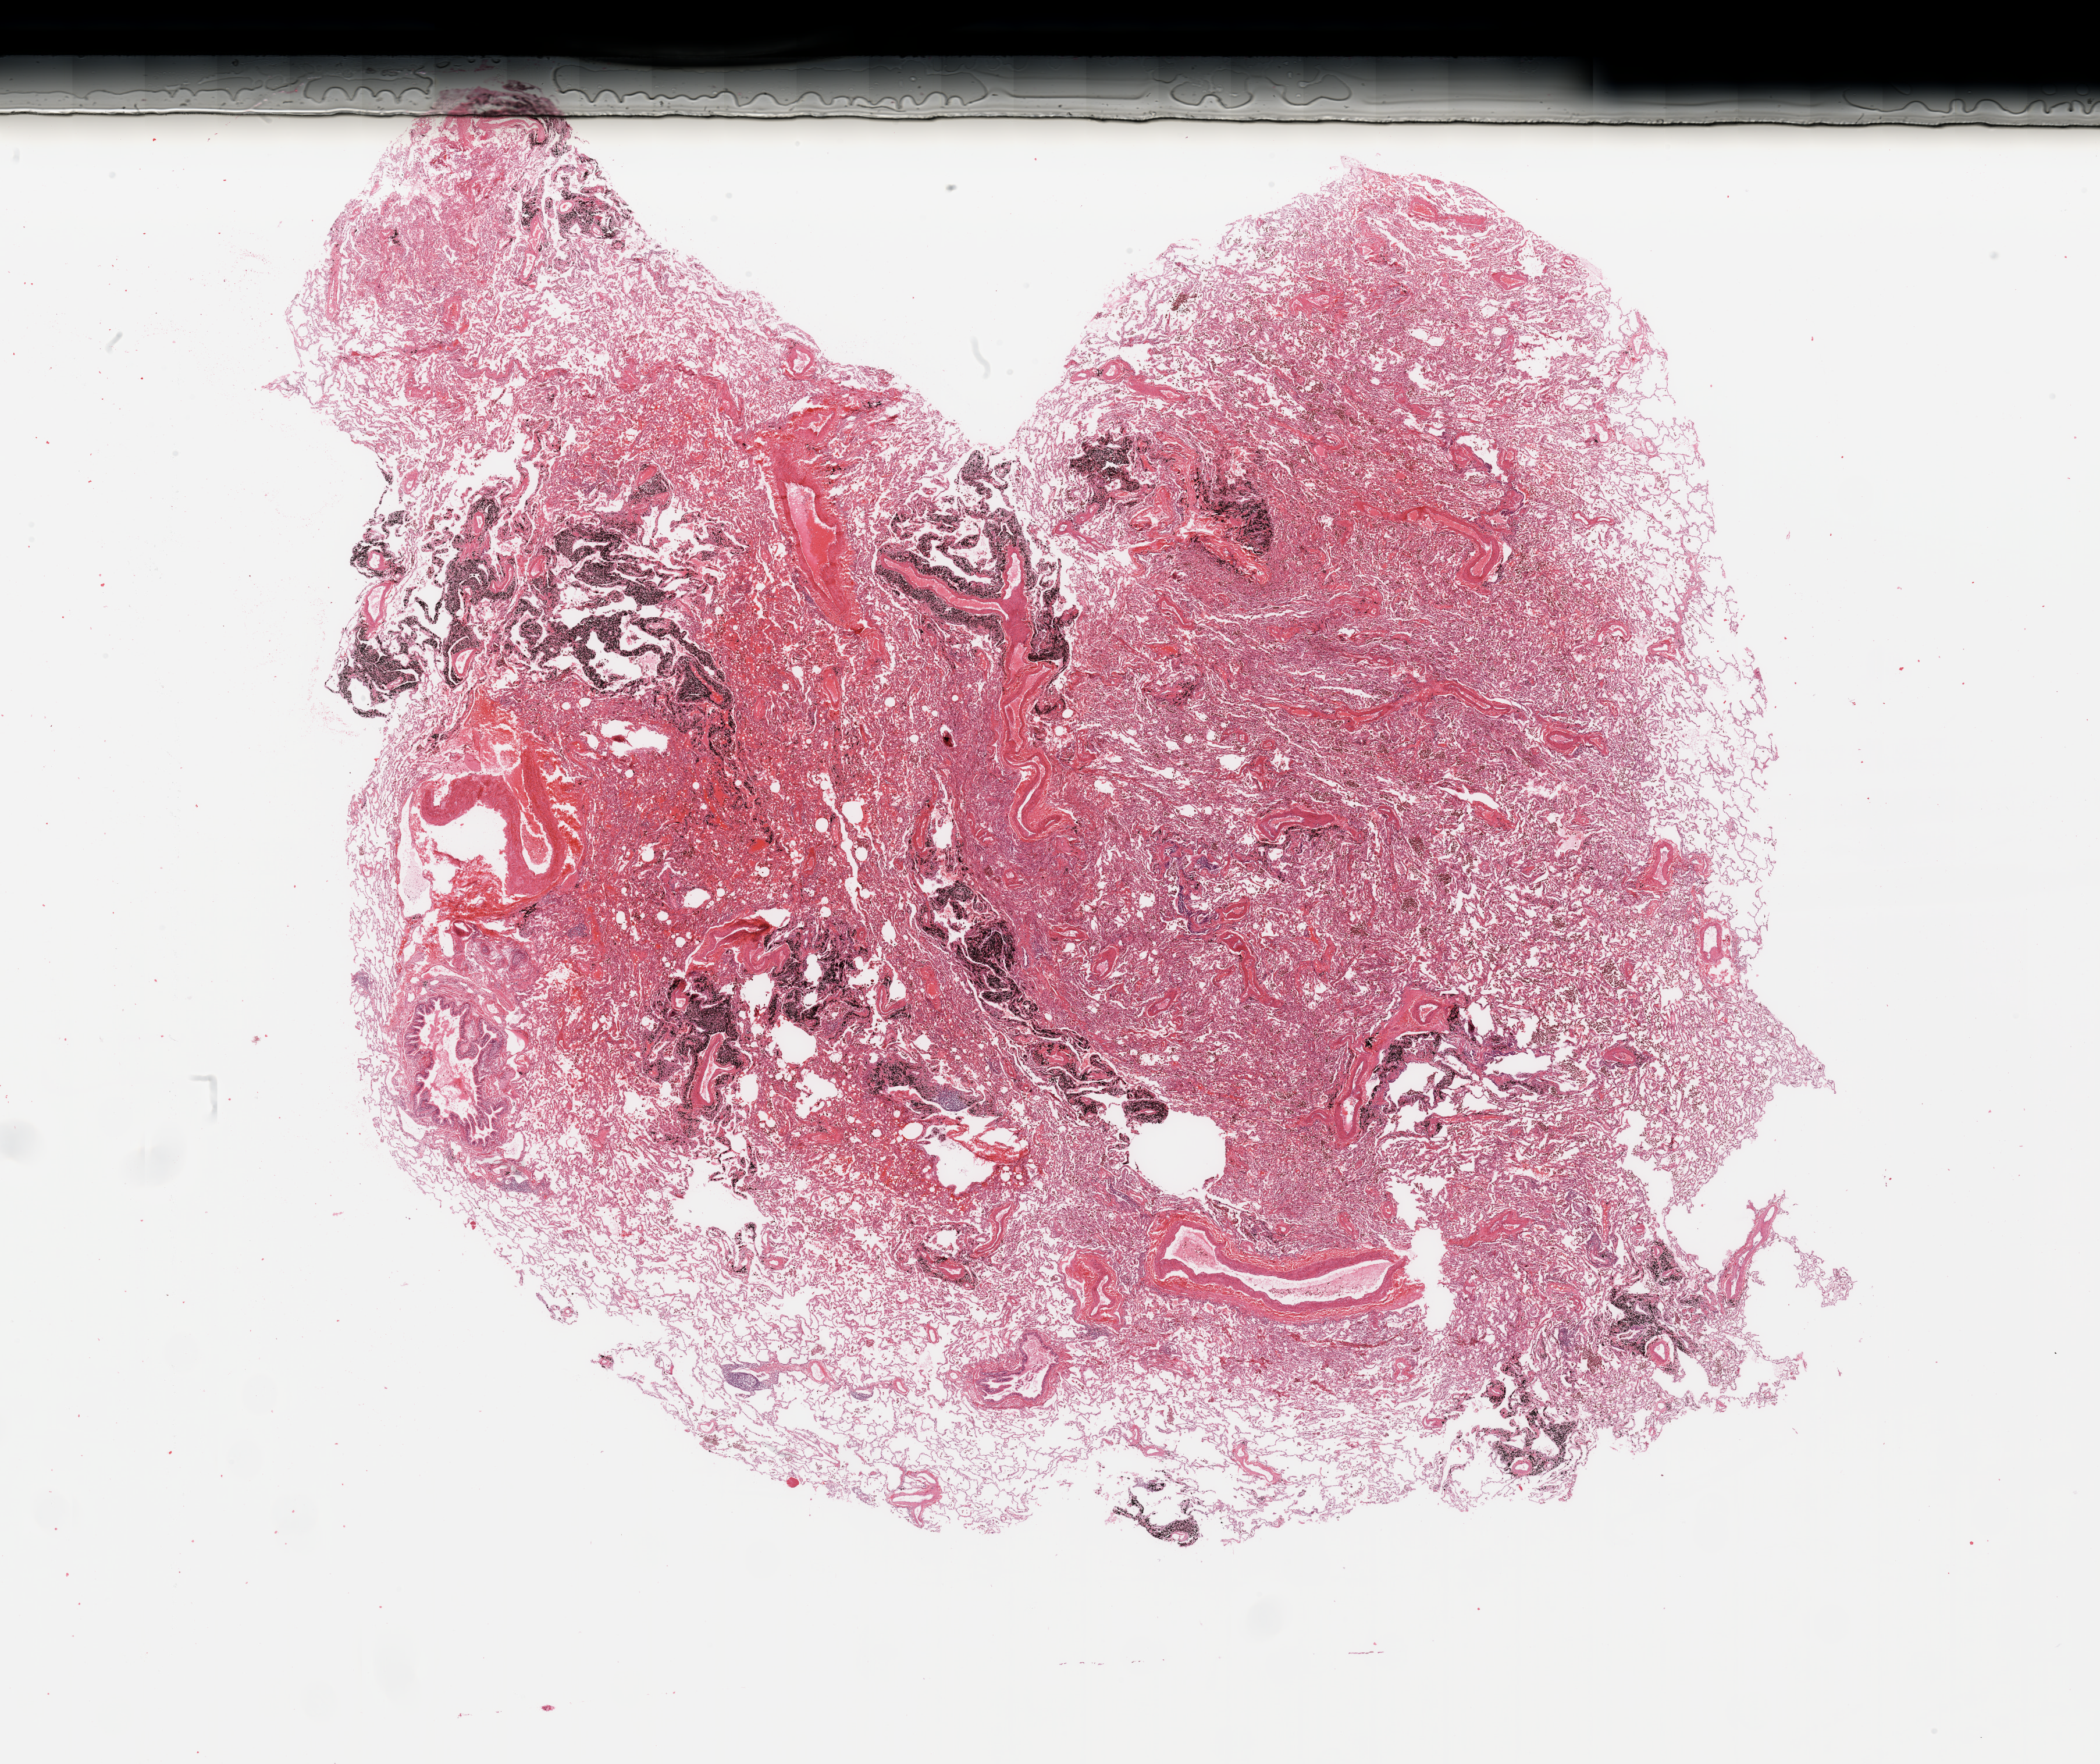
H&E-stained whole-slide image — whole scanned area (about 28.5 x 24.0 mm, slide scanned at 20x) shown as a low-resolution overview. Normal (non-tumour) tissue sample, lung. Male, 63 y/o.
This section: normal (non-tumour) tissue from the same patient. Patient diagnosis: Adenocarcinoma, NOS.